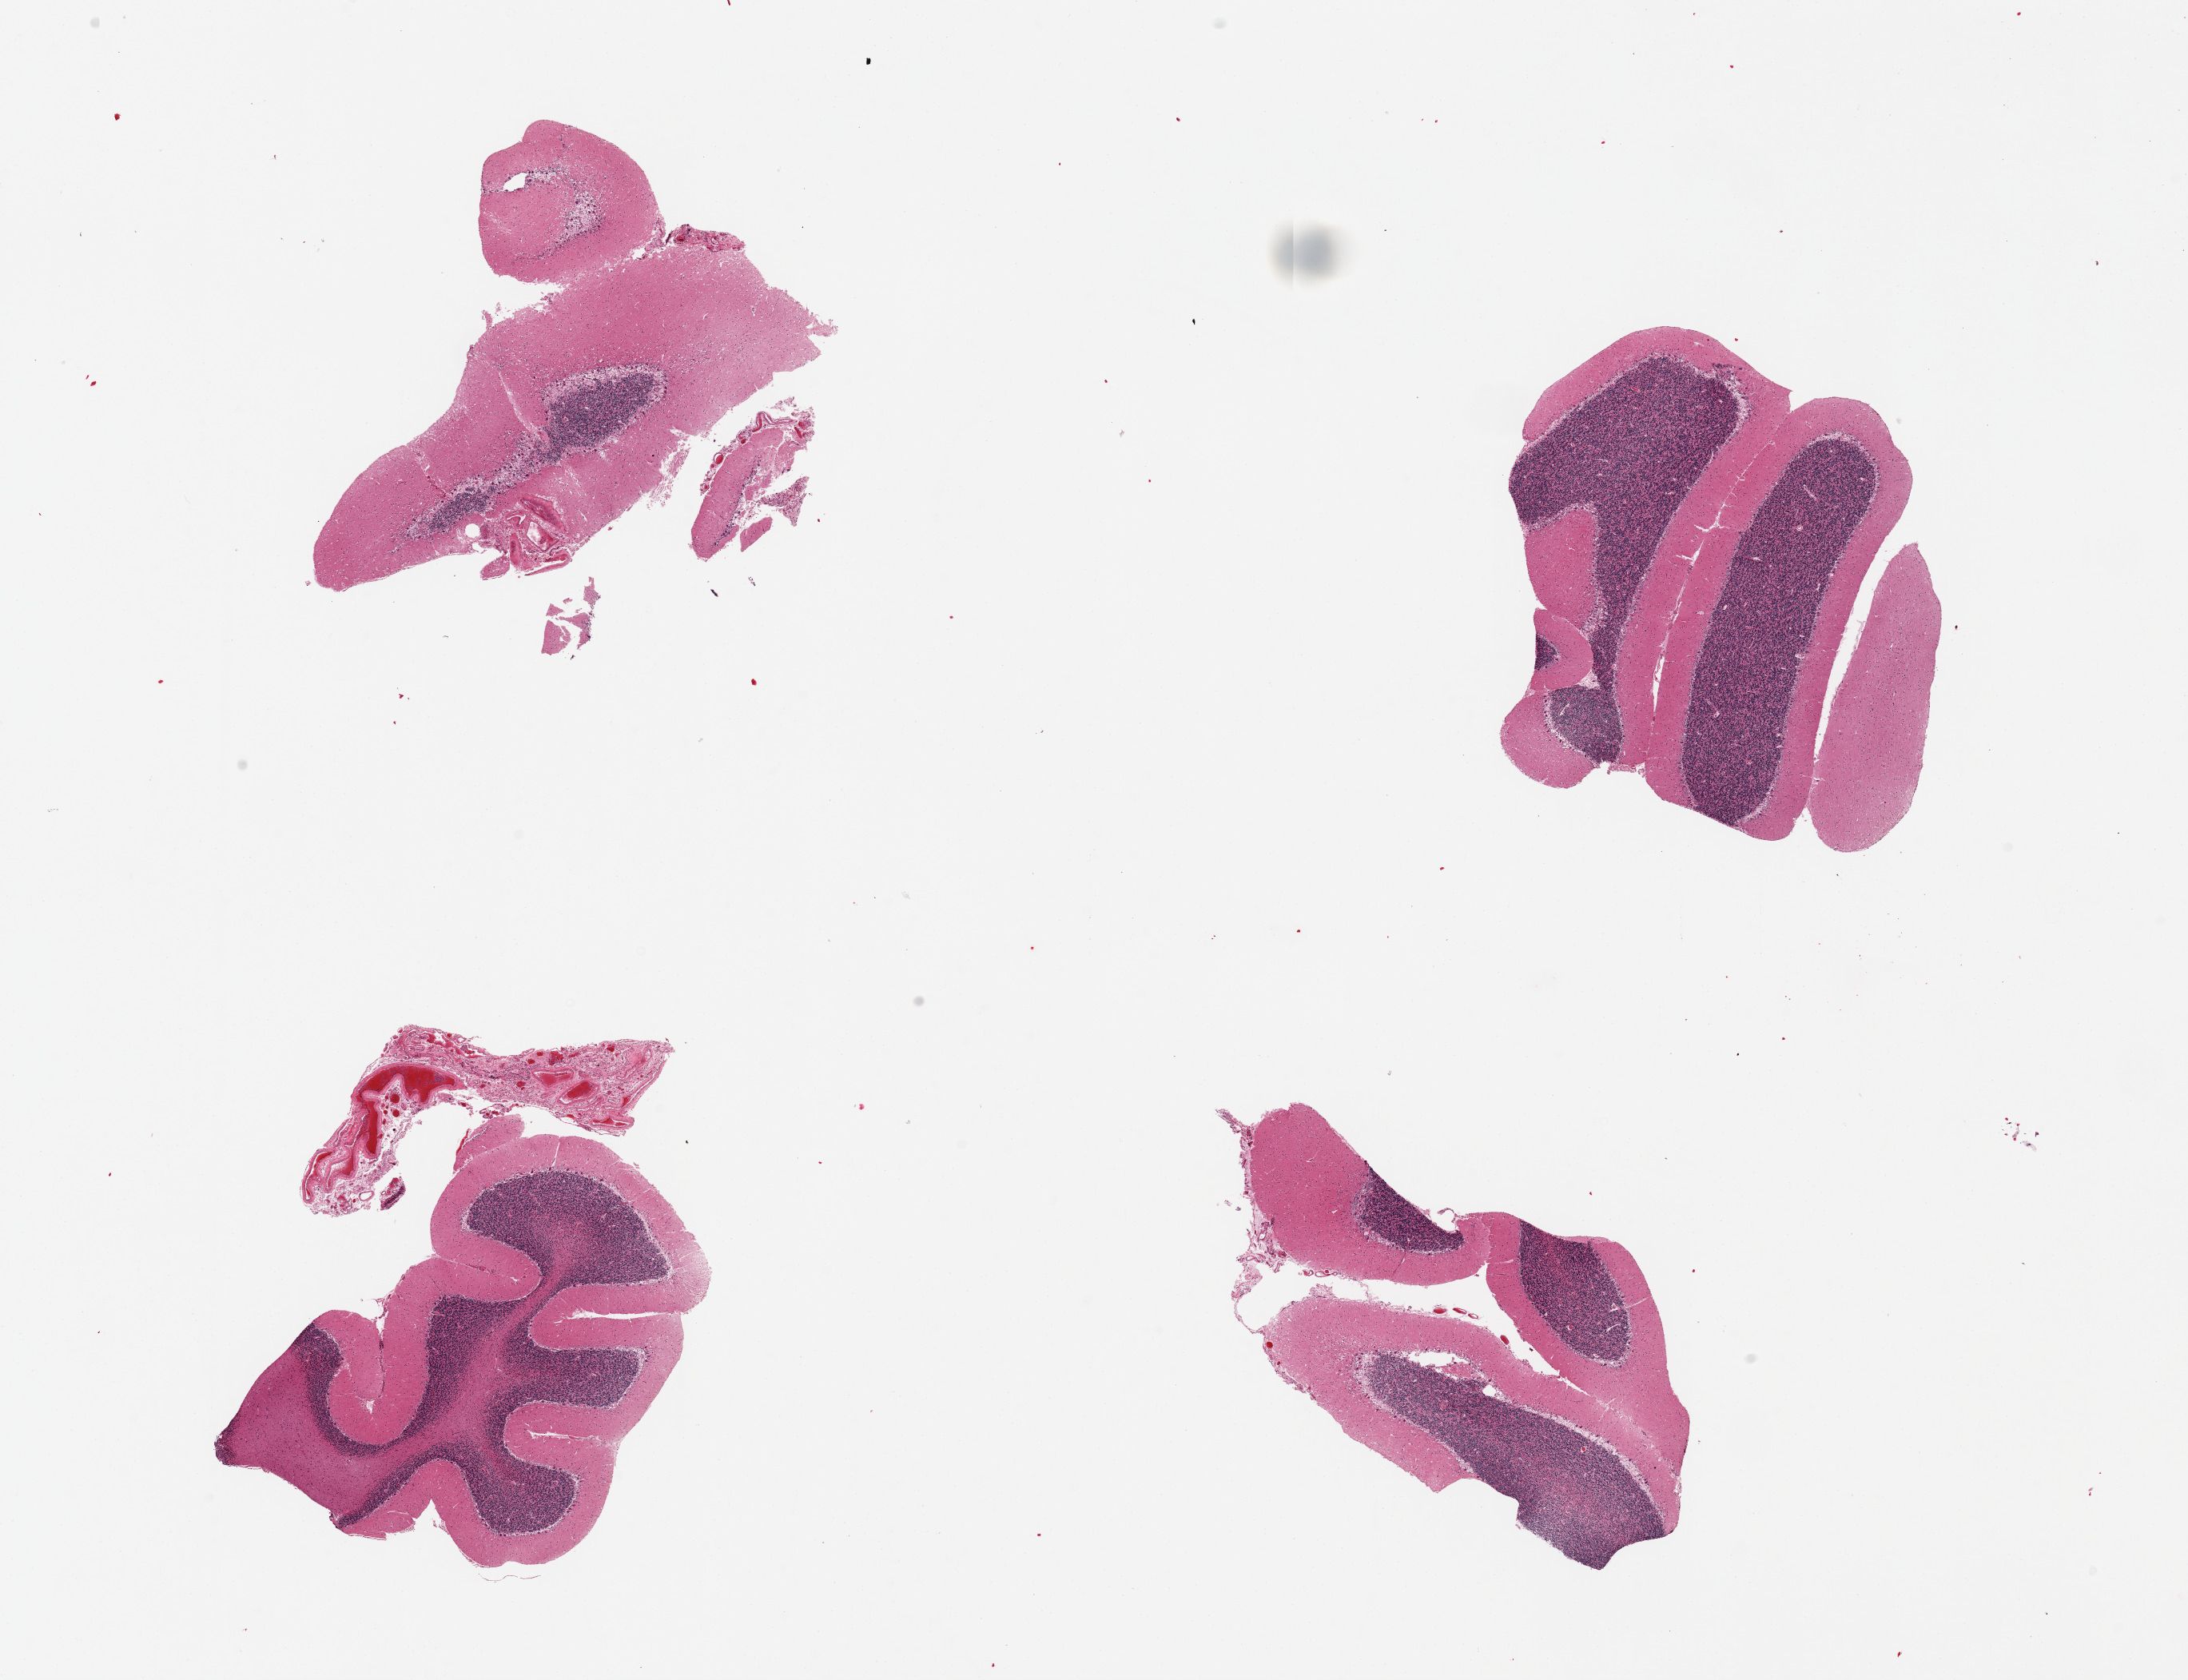
Whole-slide image, haematoxylin and eosin stain, brightfield, whole scanned area (about 21.7 x 16.6 mm) shown as a low-resolution overview. PAXgene-fixed paraffin-embedded (PFPE) section. Target tissue: cerebellum. Donor tissue sample. Female donor.
Review note (as recorded): 4 pieces.